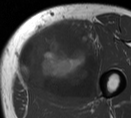
MRI of an extremity soft-tissue mass, one axial slice; position 28 of 55 along the scan axis; MR volume resampled by the dataset authors to the PET/CT grid (not the native acquisition matrix); 3.27 mm slice thickness; 131 × 118 image matrix, field of view 128 × 115 mm. Male patient. Case-level facts recorded for this patient, not image findings: histological type: pleiomorphic liposarcoma; grade: high; site of the primary tumour: left thigh.
Structures marked on this image (expert contour drawn on MRI and transferred to this co-registered scan by the dataset authors):
- gross tumour volume including surrounding oedema: bounding box (x1, y1, x2, y2) in pixels: (16, 20, 106, 104)
- gross tumour volume (mass): (16, 20, 101, 104)